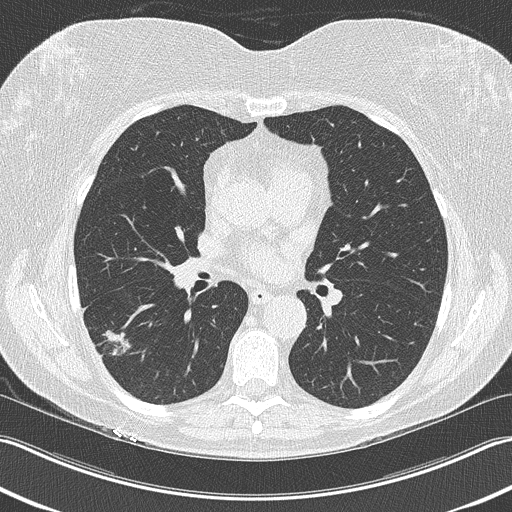
Low-dose screening chest CT, one axial slice. Position 122 of 210 along the scan axis. Reconstruction kernel B50f. Lung window (W 1500 / L -600 HU). 512 × 512 image matrix, field of view 348 × 348 mm.
Annotated regions visible in this slice (outlined manually by an expert reader):
- lesion 1 (tumor, lower lobe of right lung): box from (x=102, y=330) to (x=131, y=356) px